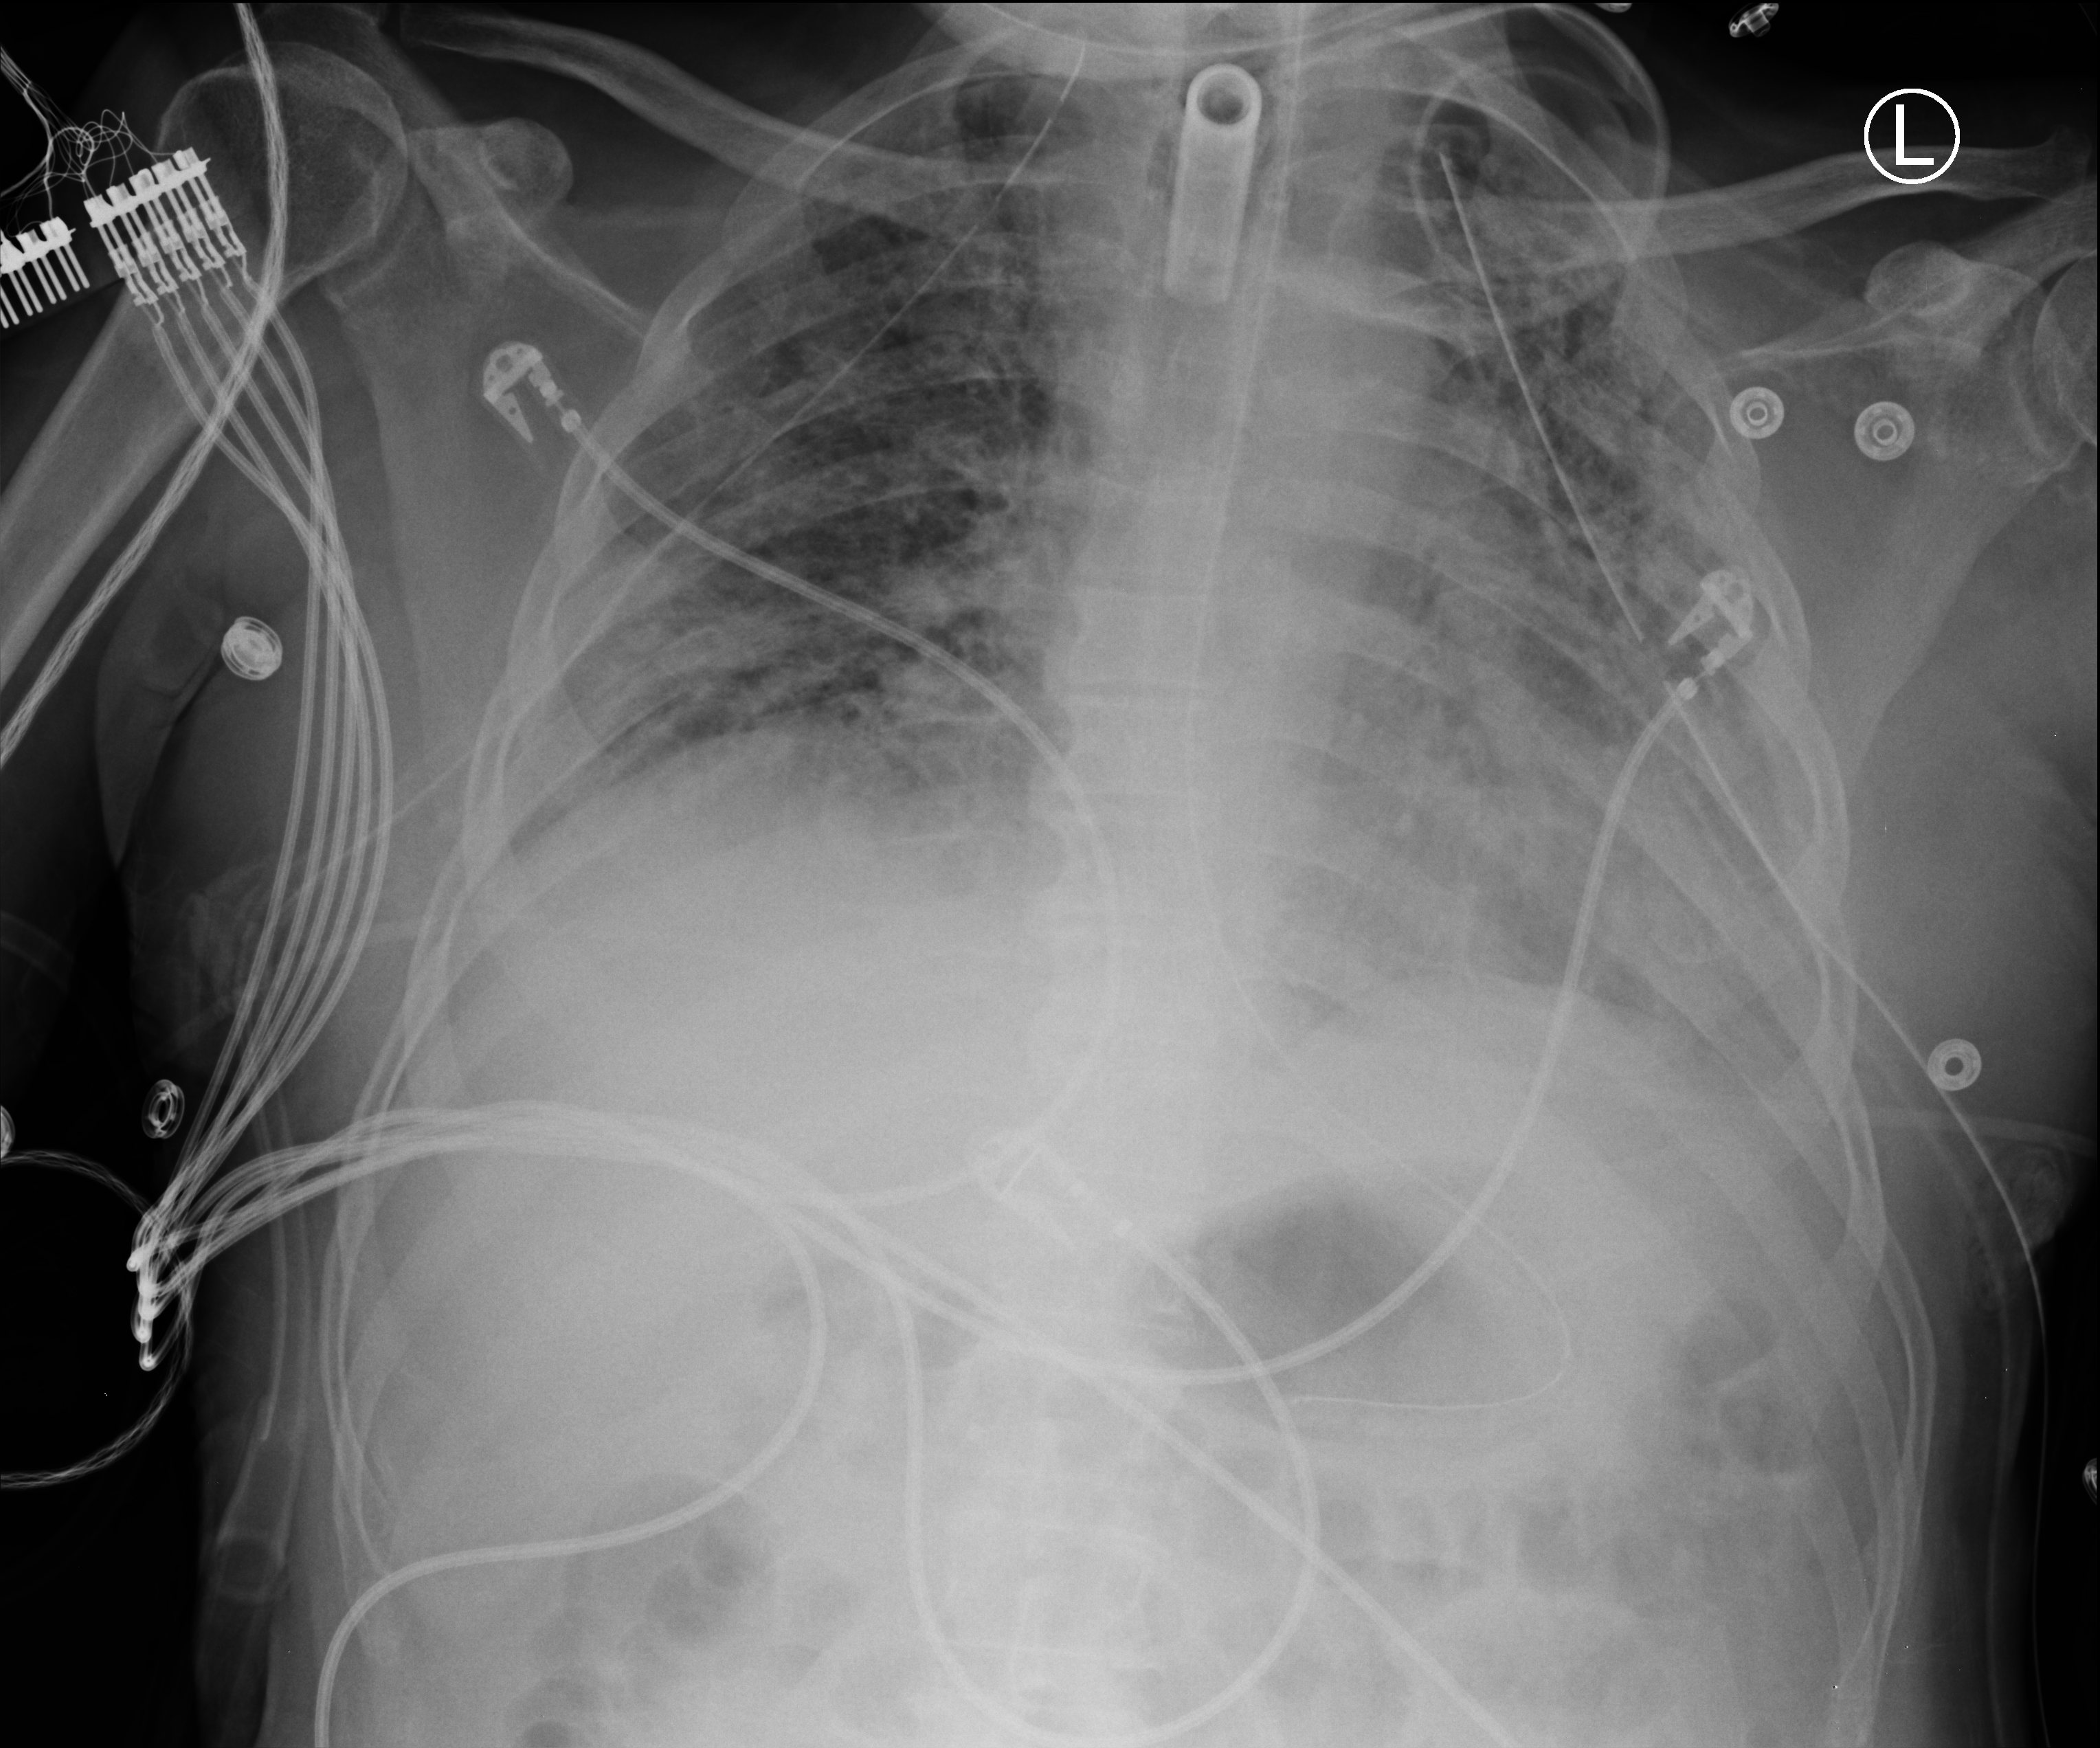
Bedside chest radiograph (computed radiography), anteroposterior (AP) projection. Male patient hospitalised with COVID-19, age 18–59 years.
From the hospital-stay record, not from the radiograph (when in the stay this image was taken is not recorded): diabetes (admission record): no; mechanically ventilated during this hospital stay: yes; admitted to intensive care during this hospital stay: yes.